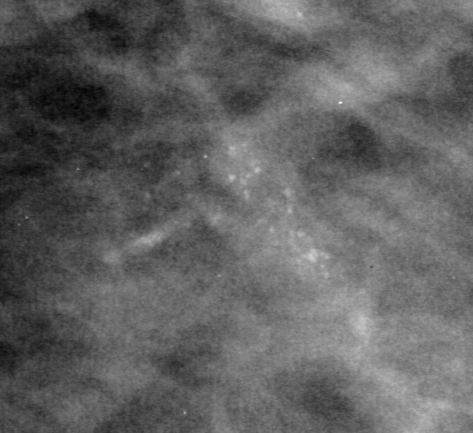
Region of interest cut from a scanned film mammogram (one marked finding), left breast, CC view, BI-RADS breast density category 3 (scale 1–4).
Marked abnormality: calcifications, morphology punctate / fine linear branching, distribution clustered; BI-RADS assessment category 0; subtlety rating 4 on a 1 (subtle) to 5 (obvious) scale; pathology result (as recorded, not read from the image): malignant.